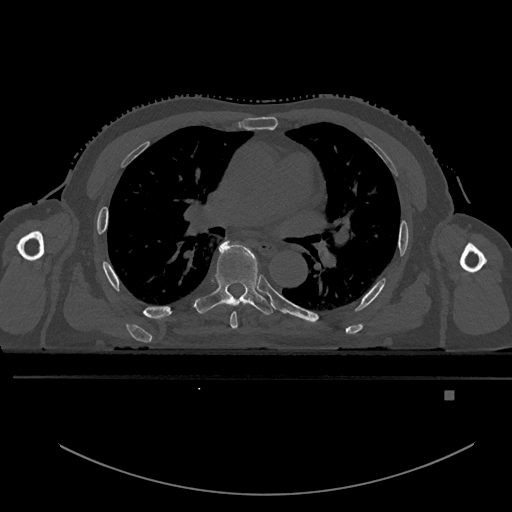
CT including the spine, one axial slice; slice 321 of 969 in the series (ordered by position); bone window (W 1800 / L 400 HU); 0.5 mm slice thickness; 512 × 512 image matrix, field of view 456 × 456 mm. Patient: male, 82 years. Case-level facts recorded for this patient, not image findings: primary cancer: prostate; vertebrae with lytic lesions (as recorded): T11, T9, T8, T2.
Annotated regions visible in this slice (semi-automatically segmented with operator editing):
- T5 vertebra: bounding box (x1, y1, x2, y2) in pixels: (229, 242, 238, 329)
- T6 vertebra: (192, 238, 274, 315)